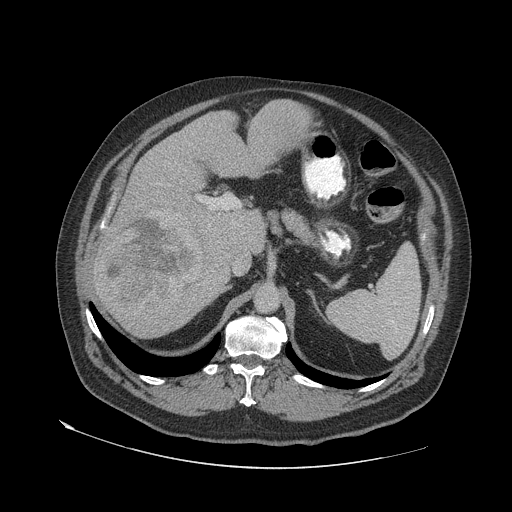
Contrast-enhanced abdominal CT (liver protocol), one axial slice. Slice 39 of 79 in the series (ordered by position). Soft-tissue window (W 400 / L 40 HU). 512 × 512 image matrix, field of view 480 × 480 mm. From the clinical record (not read from this slice): diagnosis: hepatocellular carcinoma (patient treated with transarterial chemoembolisation; whether this scan precedes or follows treatment is not stated here); TNM stage (as recorded): Stage-IVA.
Outlined on this slice (semi-automatically segmented with operator editing):
- liver parenchyma outside the tumour (the mass and vessels are separate outlines, so this box may not span the whole liver): bounding box (x1, y1, x2, y2) in pixels: (92, 100, 310, 336)
- mass: (95, 211, 203, 318)
- liver vessels: (102, 205, 241, 228)